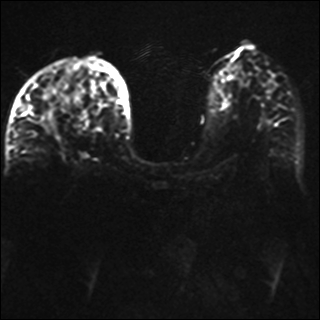
Breast MRI, one axial slice; diffusion-weighted series; image 2 of 4 stored at this slice position (different b-values; order by instance number); 1.5 T; 4 mm slice thickness; 320 × 320 image matrix, field of view 330 × 330 mm. Female patient.
Outlined on this slice (outlined manually by an expert reader):
- tumour on diffusion-weighted imaging: bounding box <41,113,55,132> (left, top, right, bottom; pixels)